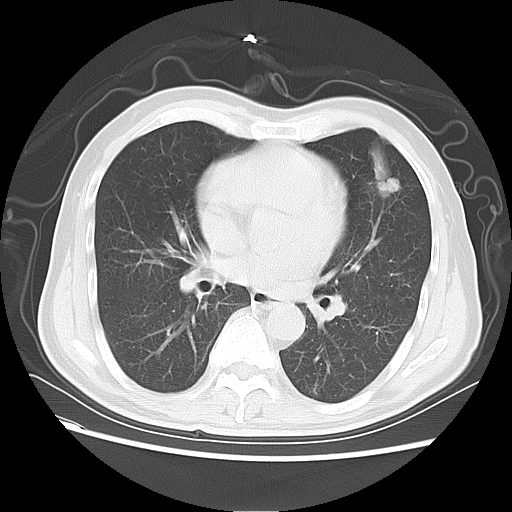
Chest CT, one axial slice. Slice 31 of 64 in the series (ordered by position). Reconstruction kernel LUNG. Lung window (W 1500 / L -600 HU). 5 mm slice thickness. 512 × 512 image matrix. Patient: male, 60 years. Case-level facts recorded for this patient, not image findings: clinical TNM (as recorded): T2a N0 M0; histopathological grade: G3.
Outlined on this slice (rectangle marked by the reading radiologist):
- lung tumour (recorded histology: adenocarcinoma): bounding box [x1, y1, x2, y2] px = [366, 145, 402, 208]